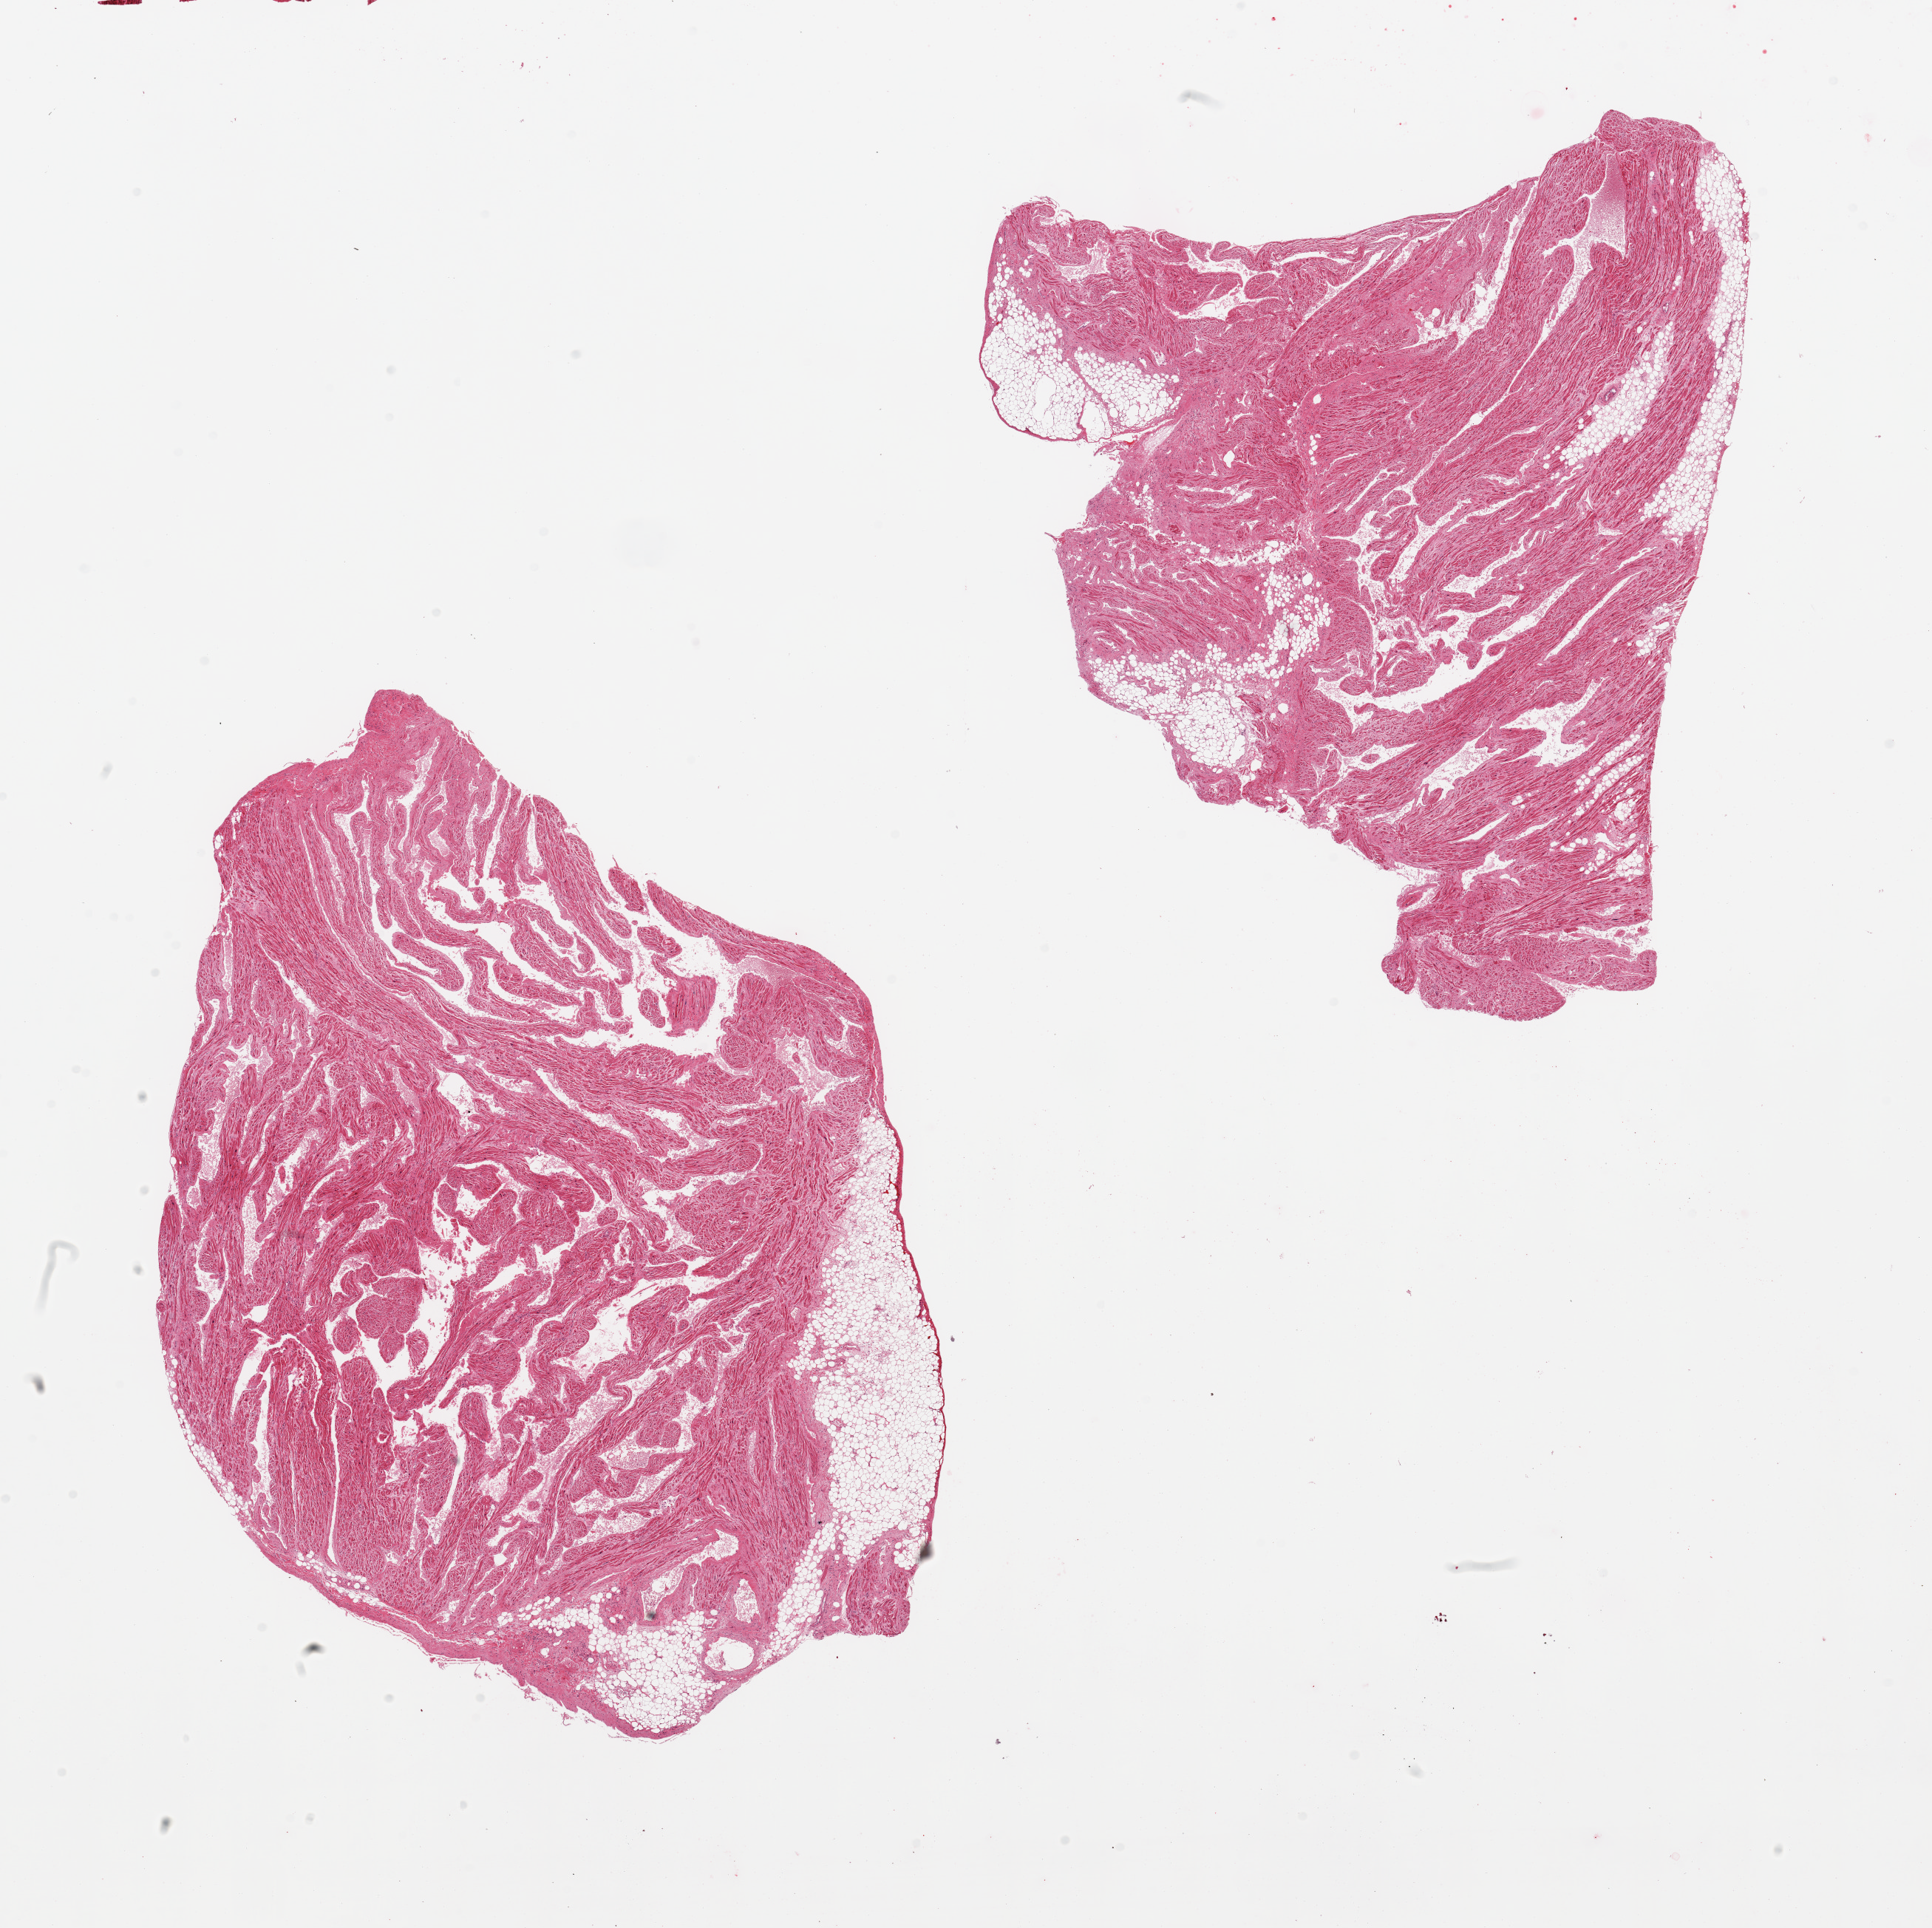
Digitized haematoxylin and eosin-stained section — a low-resolution overview of the entire scanned area, about 20.7 x 20.6 mm (acquisition: 20x scan). PAXgene-fixed, paraffin-embedded tissue. Sampled site (target tissue): auricular appendage. Tissue donor sample. Donor sex: female.
Review note (as recorded): 2 pieces; up to 20% fatty.